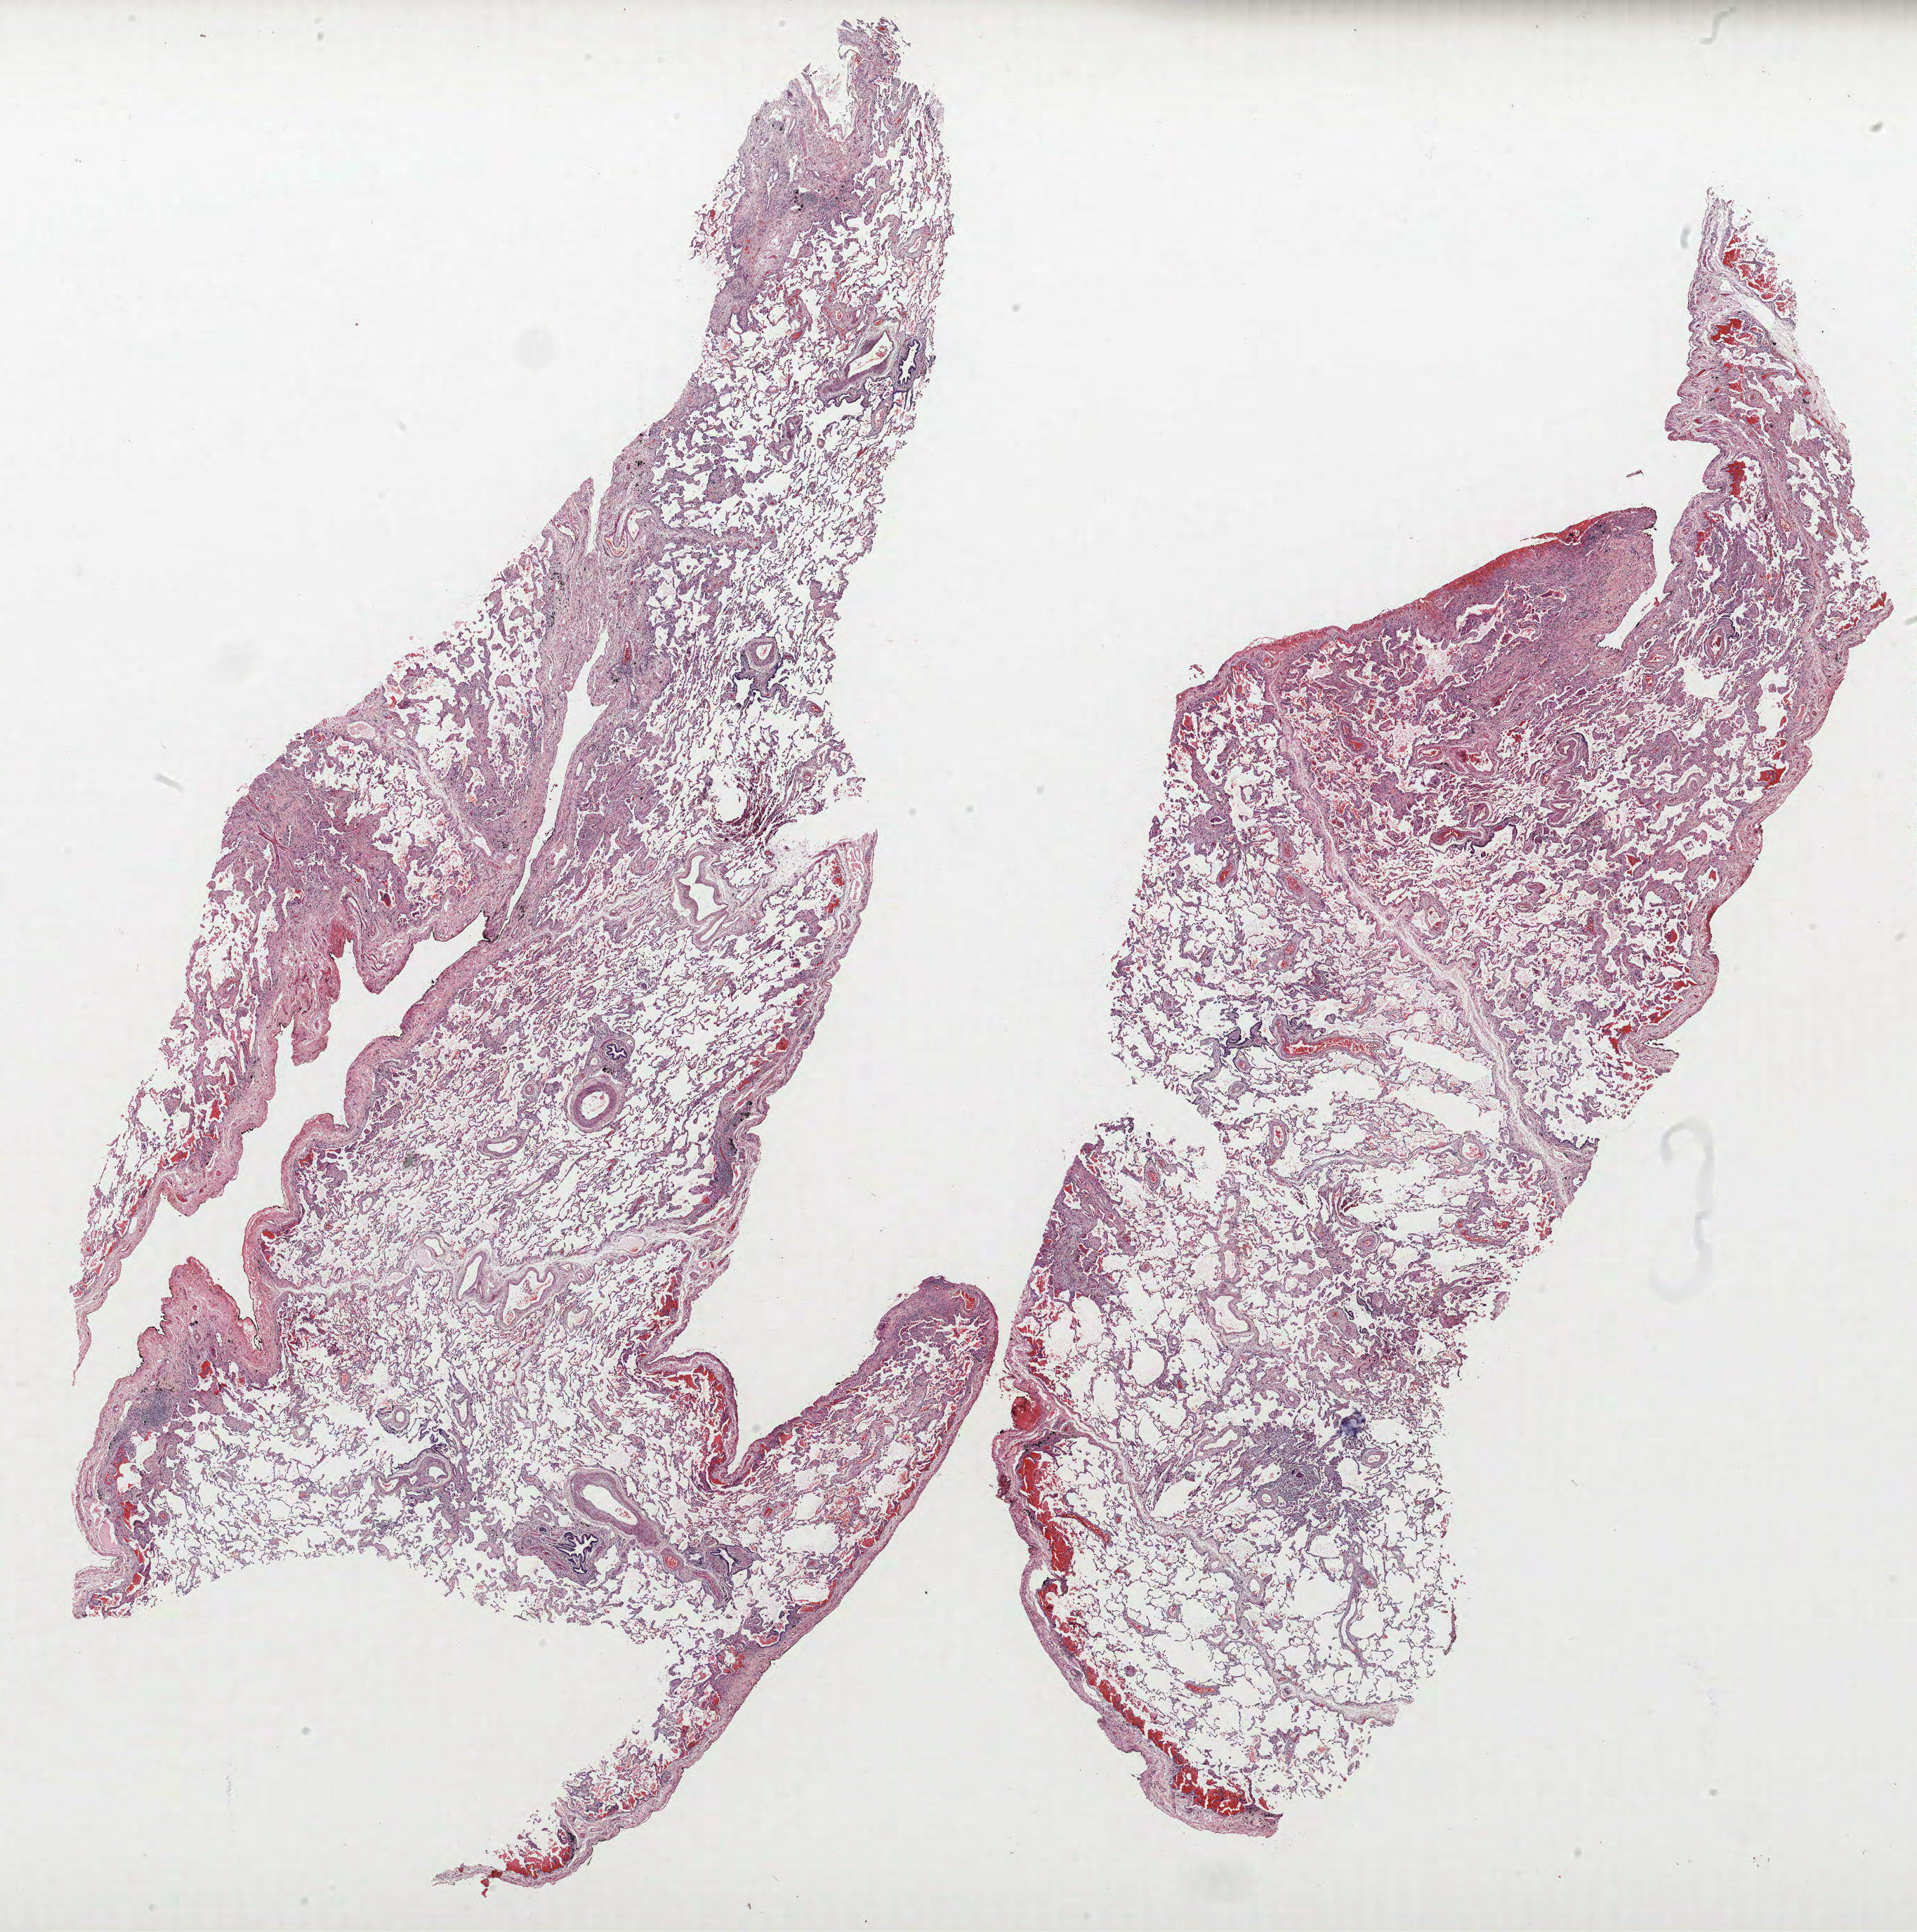
Whole-slide histology image, H&E, whole scanned area (about 21.8 x 22.0 mm) shown as a low-resolution overview. FFPE section. Lung tissue. Male, age 60 at enrolment. Former smoker at enrolment.
Tumour size (pathology): 18 mm. Primary tumour location (clinical record): right lower lobe. Participant's lung-cancer diagnosis: Adenocarcinoma, NOS (ICD-O-3 8140/3). Stage (AJCC 6th edition): IA.